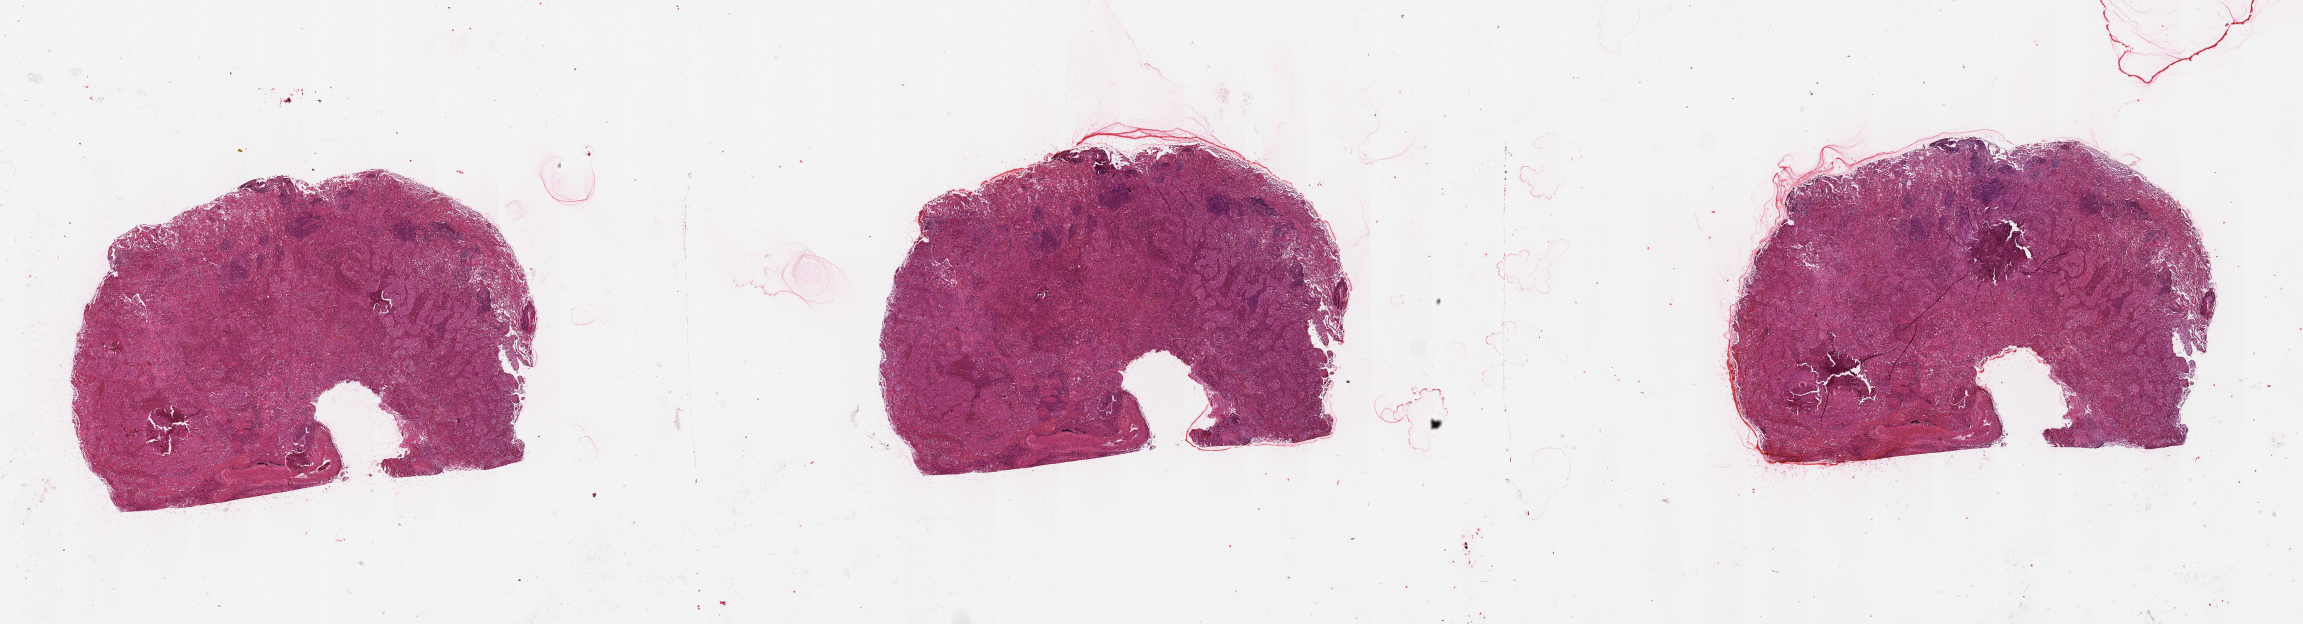
Digitized H&E-stained tissue section (whole slide) — a low-resolution overview of the entire scanned area, about 37.1 x 10.0 mm (acquisition: 20x scan). Lung, tissue type not recorded.
Patient diagnosis (cohort enrolment): squamous cell carcinoma (lung).